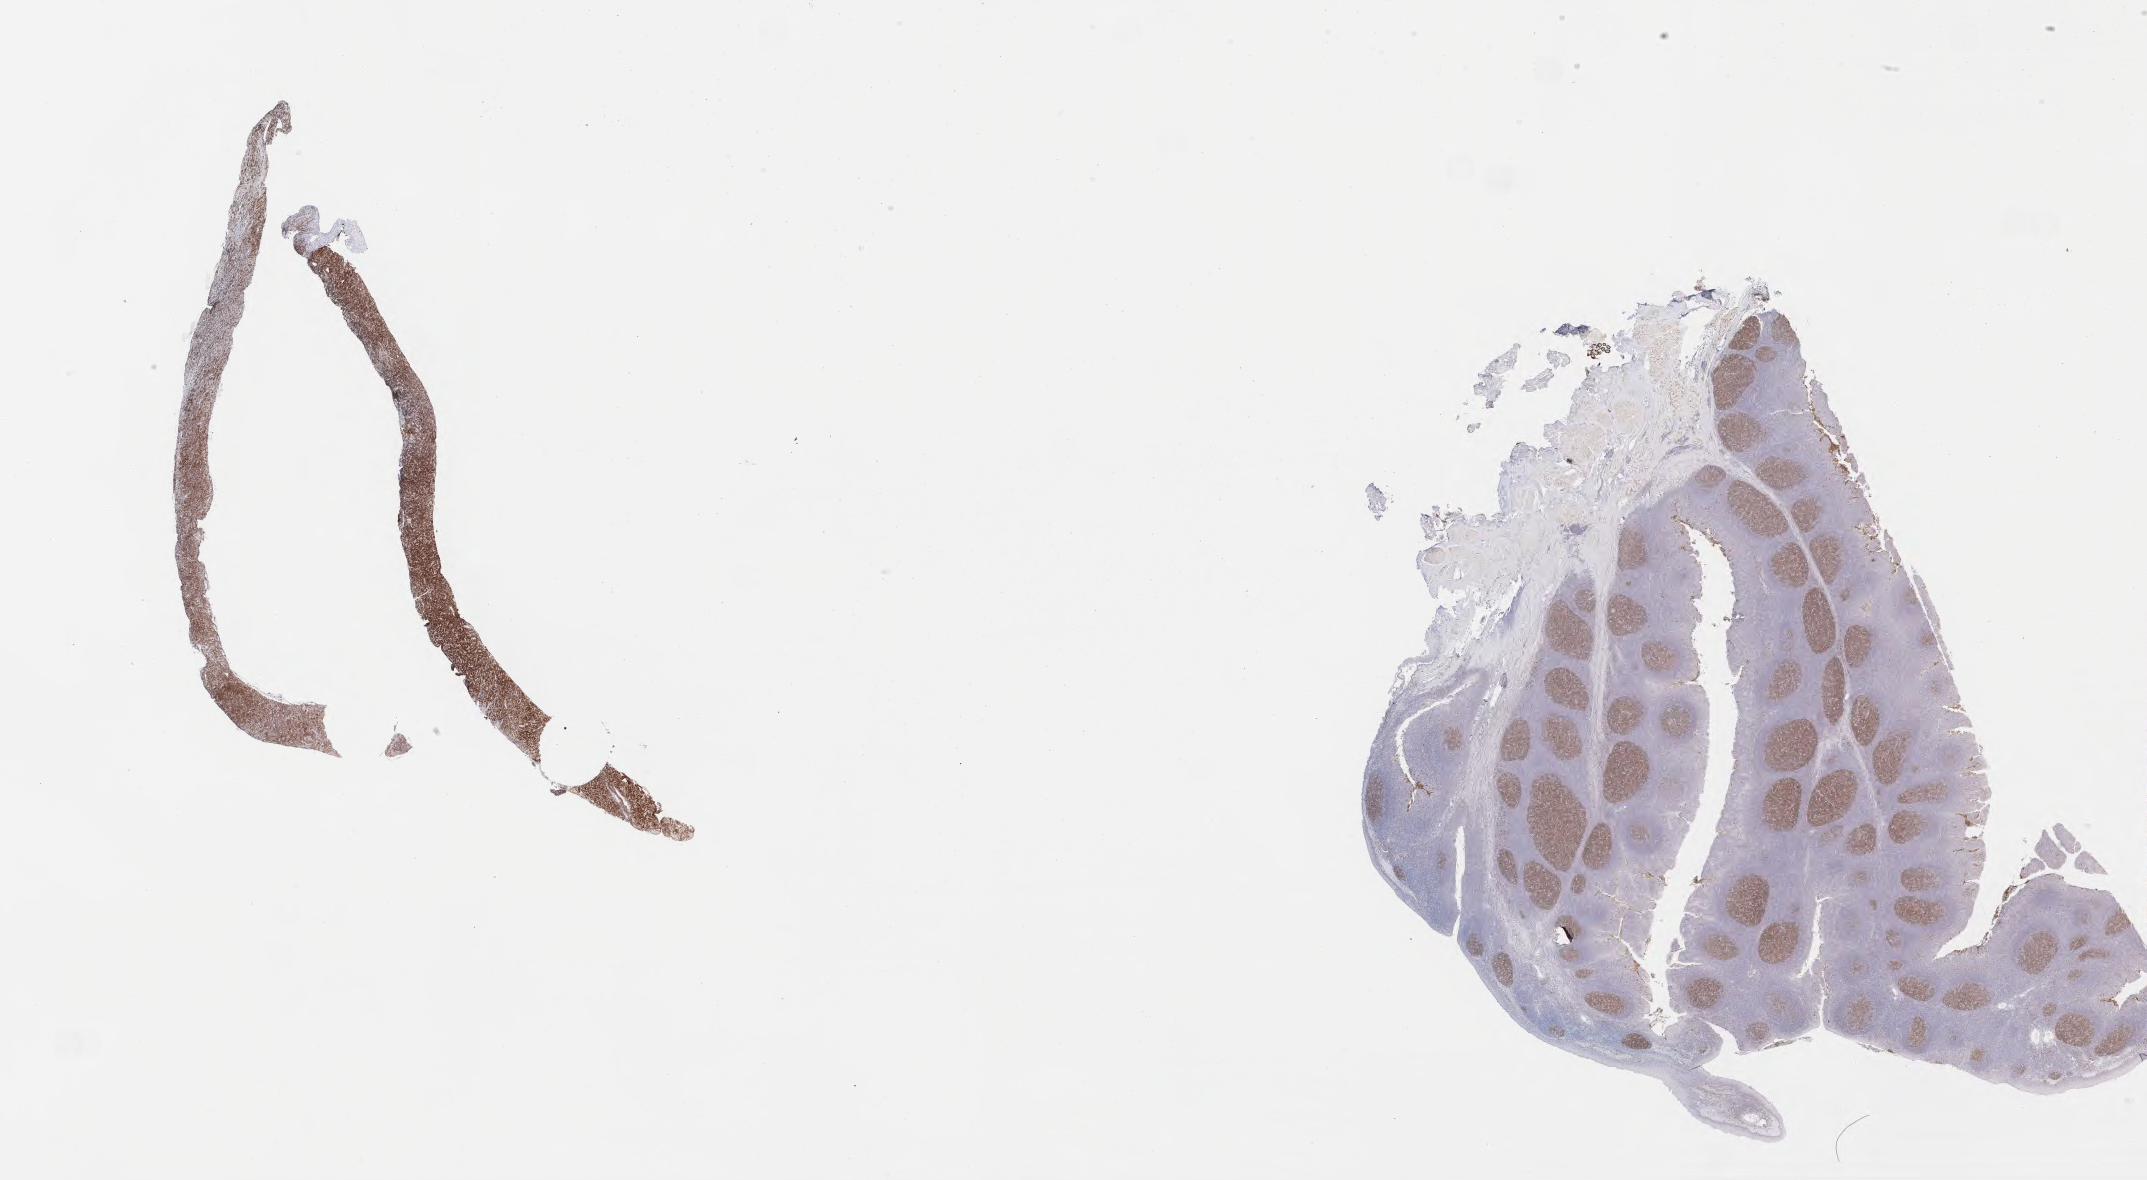
IHC for CD10, whole-slide image, whole scanned area (about 34.7 x 19.1 mm) shown as a low-resolution overview. Tumor tissue. Anatomic site: abdomen proper. Patient: male, age at initial diagnosis 9 years.
* histologic diagnosis: Burkitt lymphoma, NOS